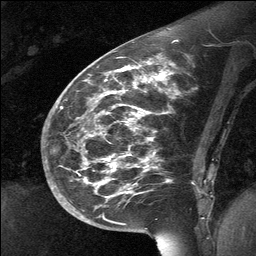
Breast MRI (dynamic contrast-enhanced), one sagittal slice; slice 26 of 64 in the series (ordered by position); dynamic contrast-enhanced study with each time point stored as its own series, time point 2 of 3 at this slice position (early post-contrast, ordered by acquisition time); 1.5 T; TE 4.8 ms, TR 27 ms; 256 × 256 image matrix, field of view 200 × 200 mm. Patient: female, 39 years. Case-level facts recorded for this patient, not image findings: setting: breast cancer imaged before/during neoadjuvant chemotherapy; receptor status: HER2-positive.
Outlined on this slice (semi-automatic segmentation, software-assisted and operator-edited):
- analysis volume of interest (the breast-tissue region the enhancement analysis was run in; not a lesion): box from (x=70, y=69) to (x=202, y=224) px
- tumour enhancement mask (voxels above the 90 % enhancement threshold inside the analysis volume of interest): (x=99, y=69)–(x=126, y=185)